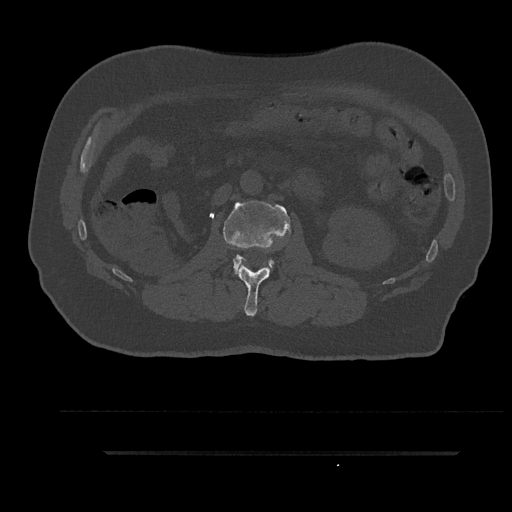
CT including the spine, one axial slice. Position 141 of 797 along the scan axis. Reconstruction kernel Br40s/3. 120 kVp. Bone window (W 1800 / L 400 HU). 0.5 mm slice thickness. 512 × 512 image matrix. Male patient, age 63 years. Case-level facts recorded for this patient, not image findings: primary cancer: renal; vertebrae with lytic lesions (as recorded): T8.
Annotated regions visible in this slice (semi-automatically segmented with operator editing):
- L1 vertebra: bounding box [x1, y1, x2, y2] px = [236, 264, 272, 316]
- L2 vertebra: [223, 201, 291, 272]